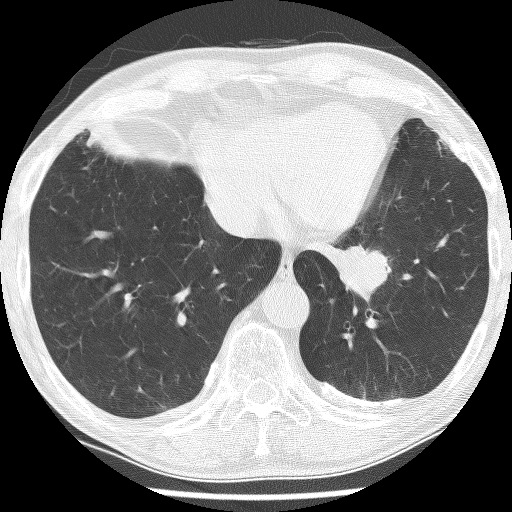
Chest CT (low-dose screening protocol), one axial image. First (baseline) screen. Lung window (W 1500 / L -600 HU). 512 × 512 image matrix. Male, age 74 years at enrolment.
Lesion marked by an expert reader, bounding box (x1, y1, x2, y2) in pixels: (314, 220, 417, 312). The exam's reader record, not a measurement of the box and not confirmed to be the same lesion: non-calcified nodule or mass ≥4 mm, left lower lobe, 30 × 27 mm, spiculated (stellate) margins, soft tissue attenuation. Official screen result: positive, change unspecified: nodule(s) >= 4 mm or enlarging nodule(s), mass(es), or other non-specific abnormalities suspicious for lung cancer. Later outcome: lung cancer diagnosed 151 days after this screen — adenocarcinoma, NOS, left lower lobe, stage IIIA (AJCC 6th edition), 49 mm at pathology.